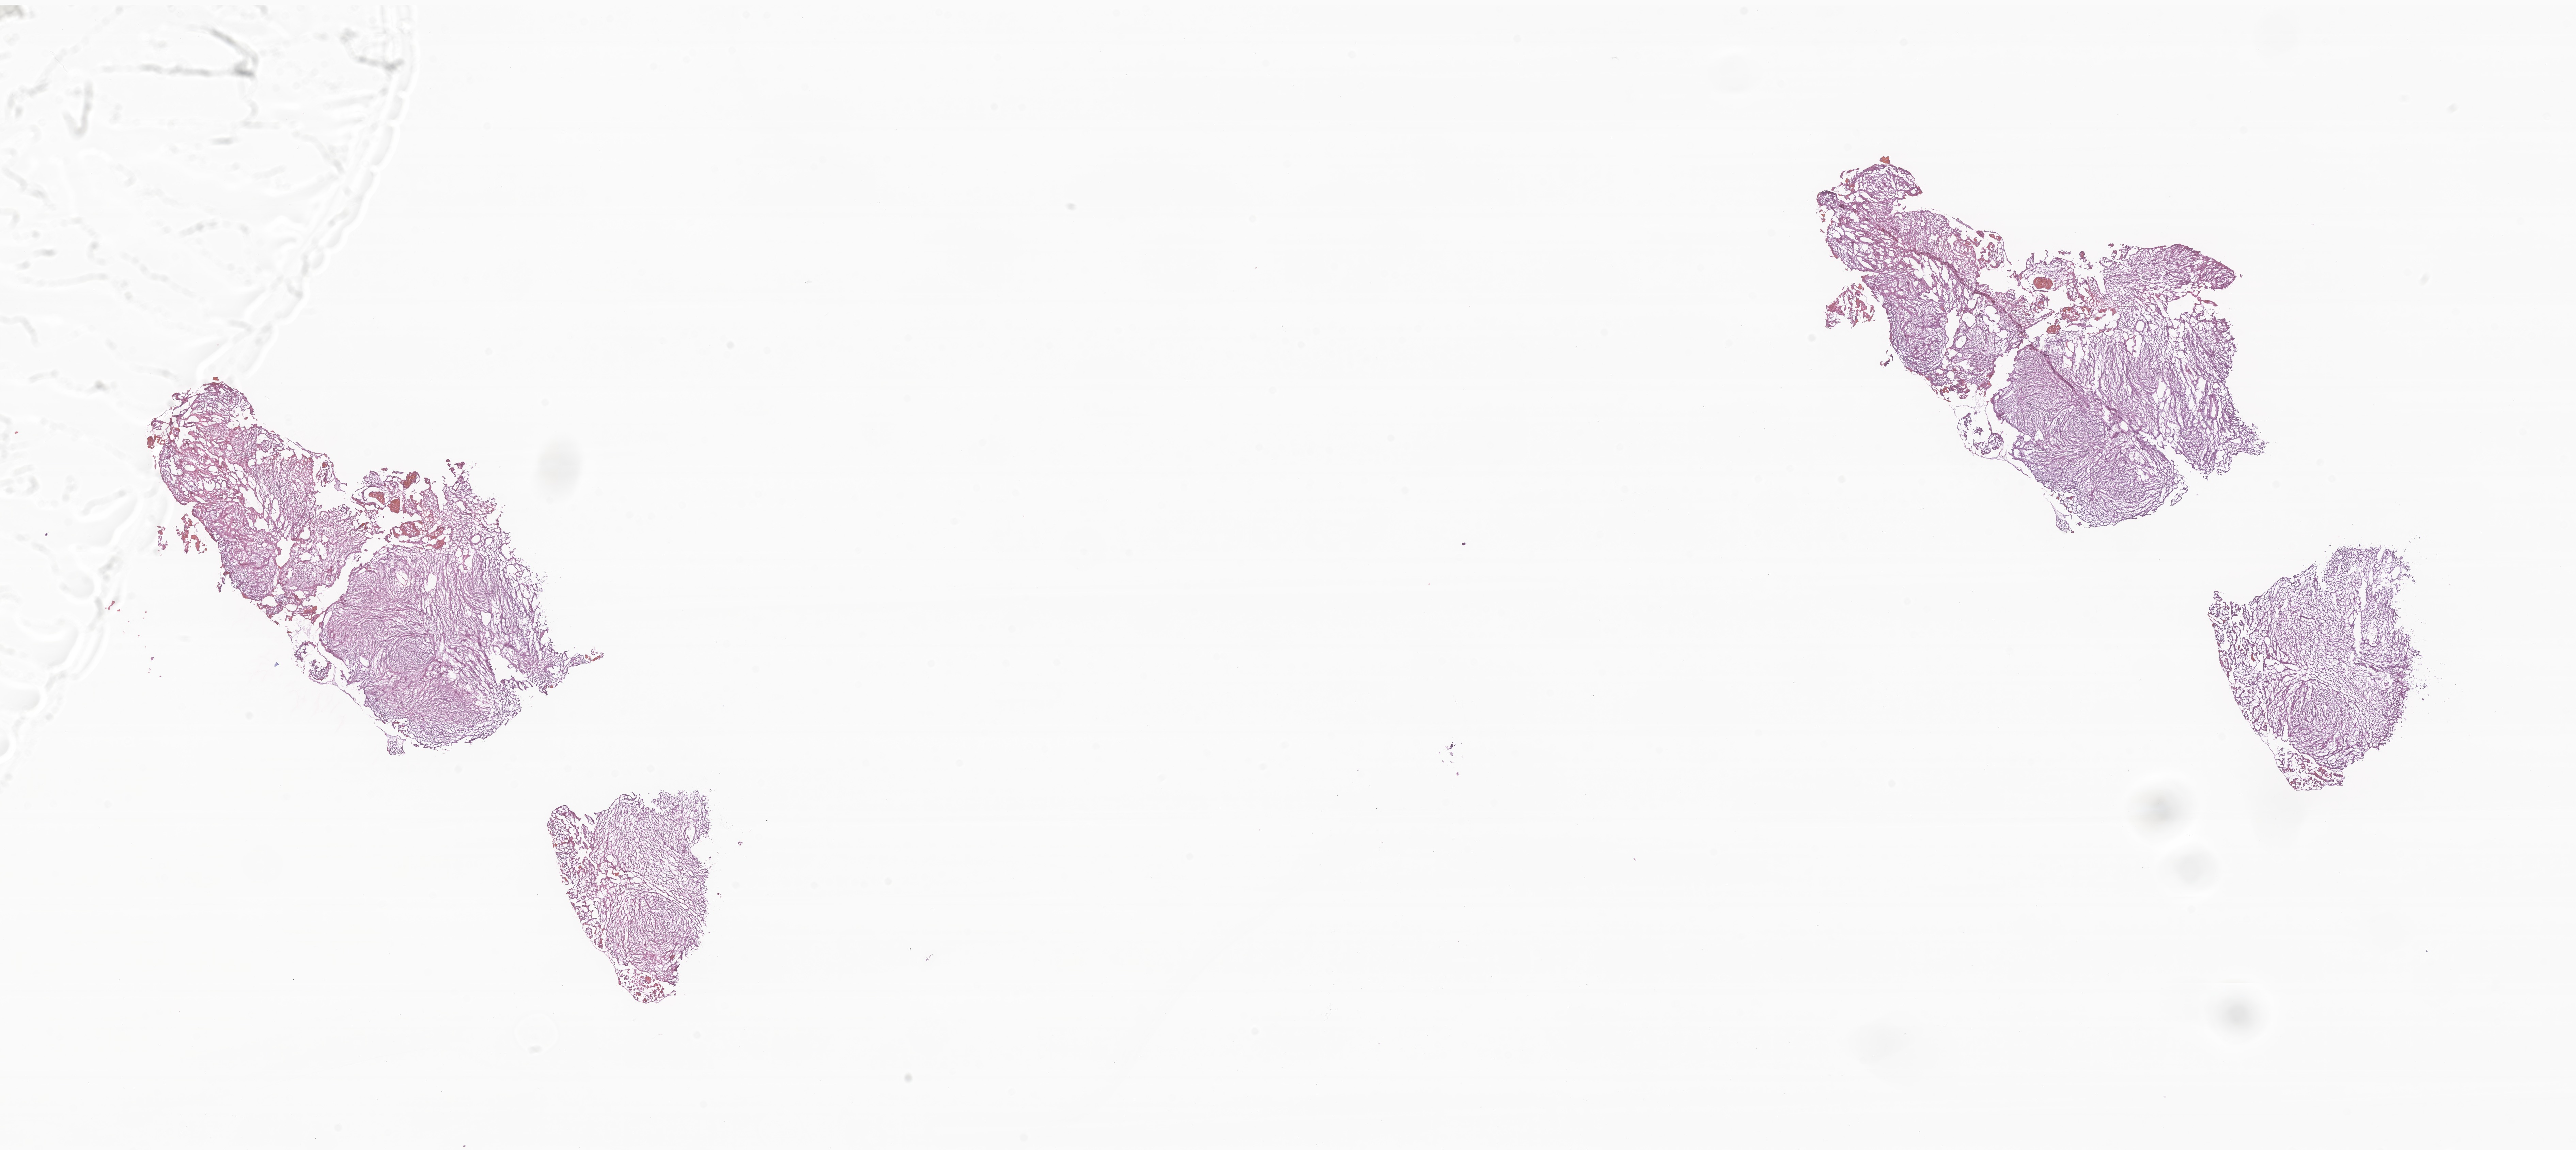
H&E whole-slide image of tumor tissue from the brain — low-resolution overview of the scanned area, about 31.9 x 14.2 mm. Frozen section. Patient female; age 173 months.
Recorded diagnosis: Neoplasm, uncertain whether benign or malignant.